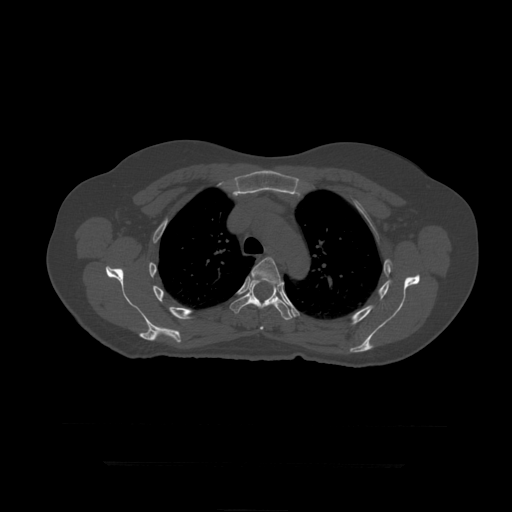
CT including the spine, one axial slice; slice 326 of 399 in the series (ordered by position); reconstruction kernel STANDARD; bone window (W 1800 / L 400 HU); 1.25 mm slice thickness; 512 × 512 image matrix, field of view 450 × 450 mm. Patient age 41 years. From the clinical record (not read from this slice): primary cancer: breast.
Structures marked on this image (semi-automatically segmented with operator editing):
- T5 vertebra: bounding box (x1, y1, x2, y2) in pixels: (251, 257, 281, 330)
- T6 vertebra: (230, 278, 297, 320)